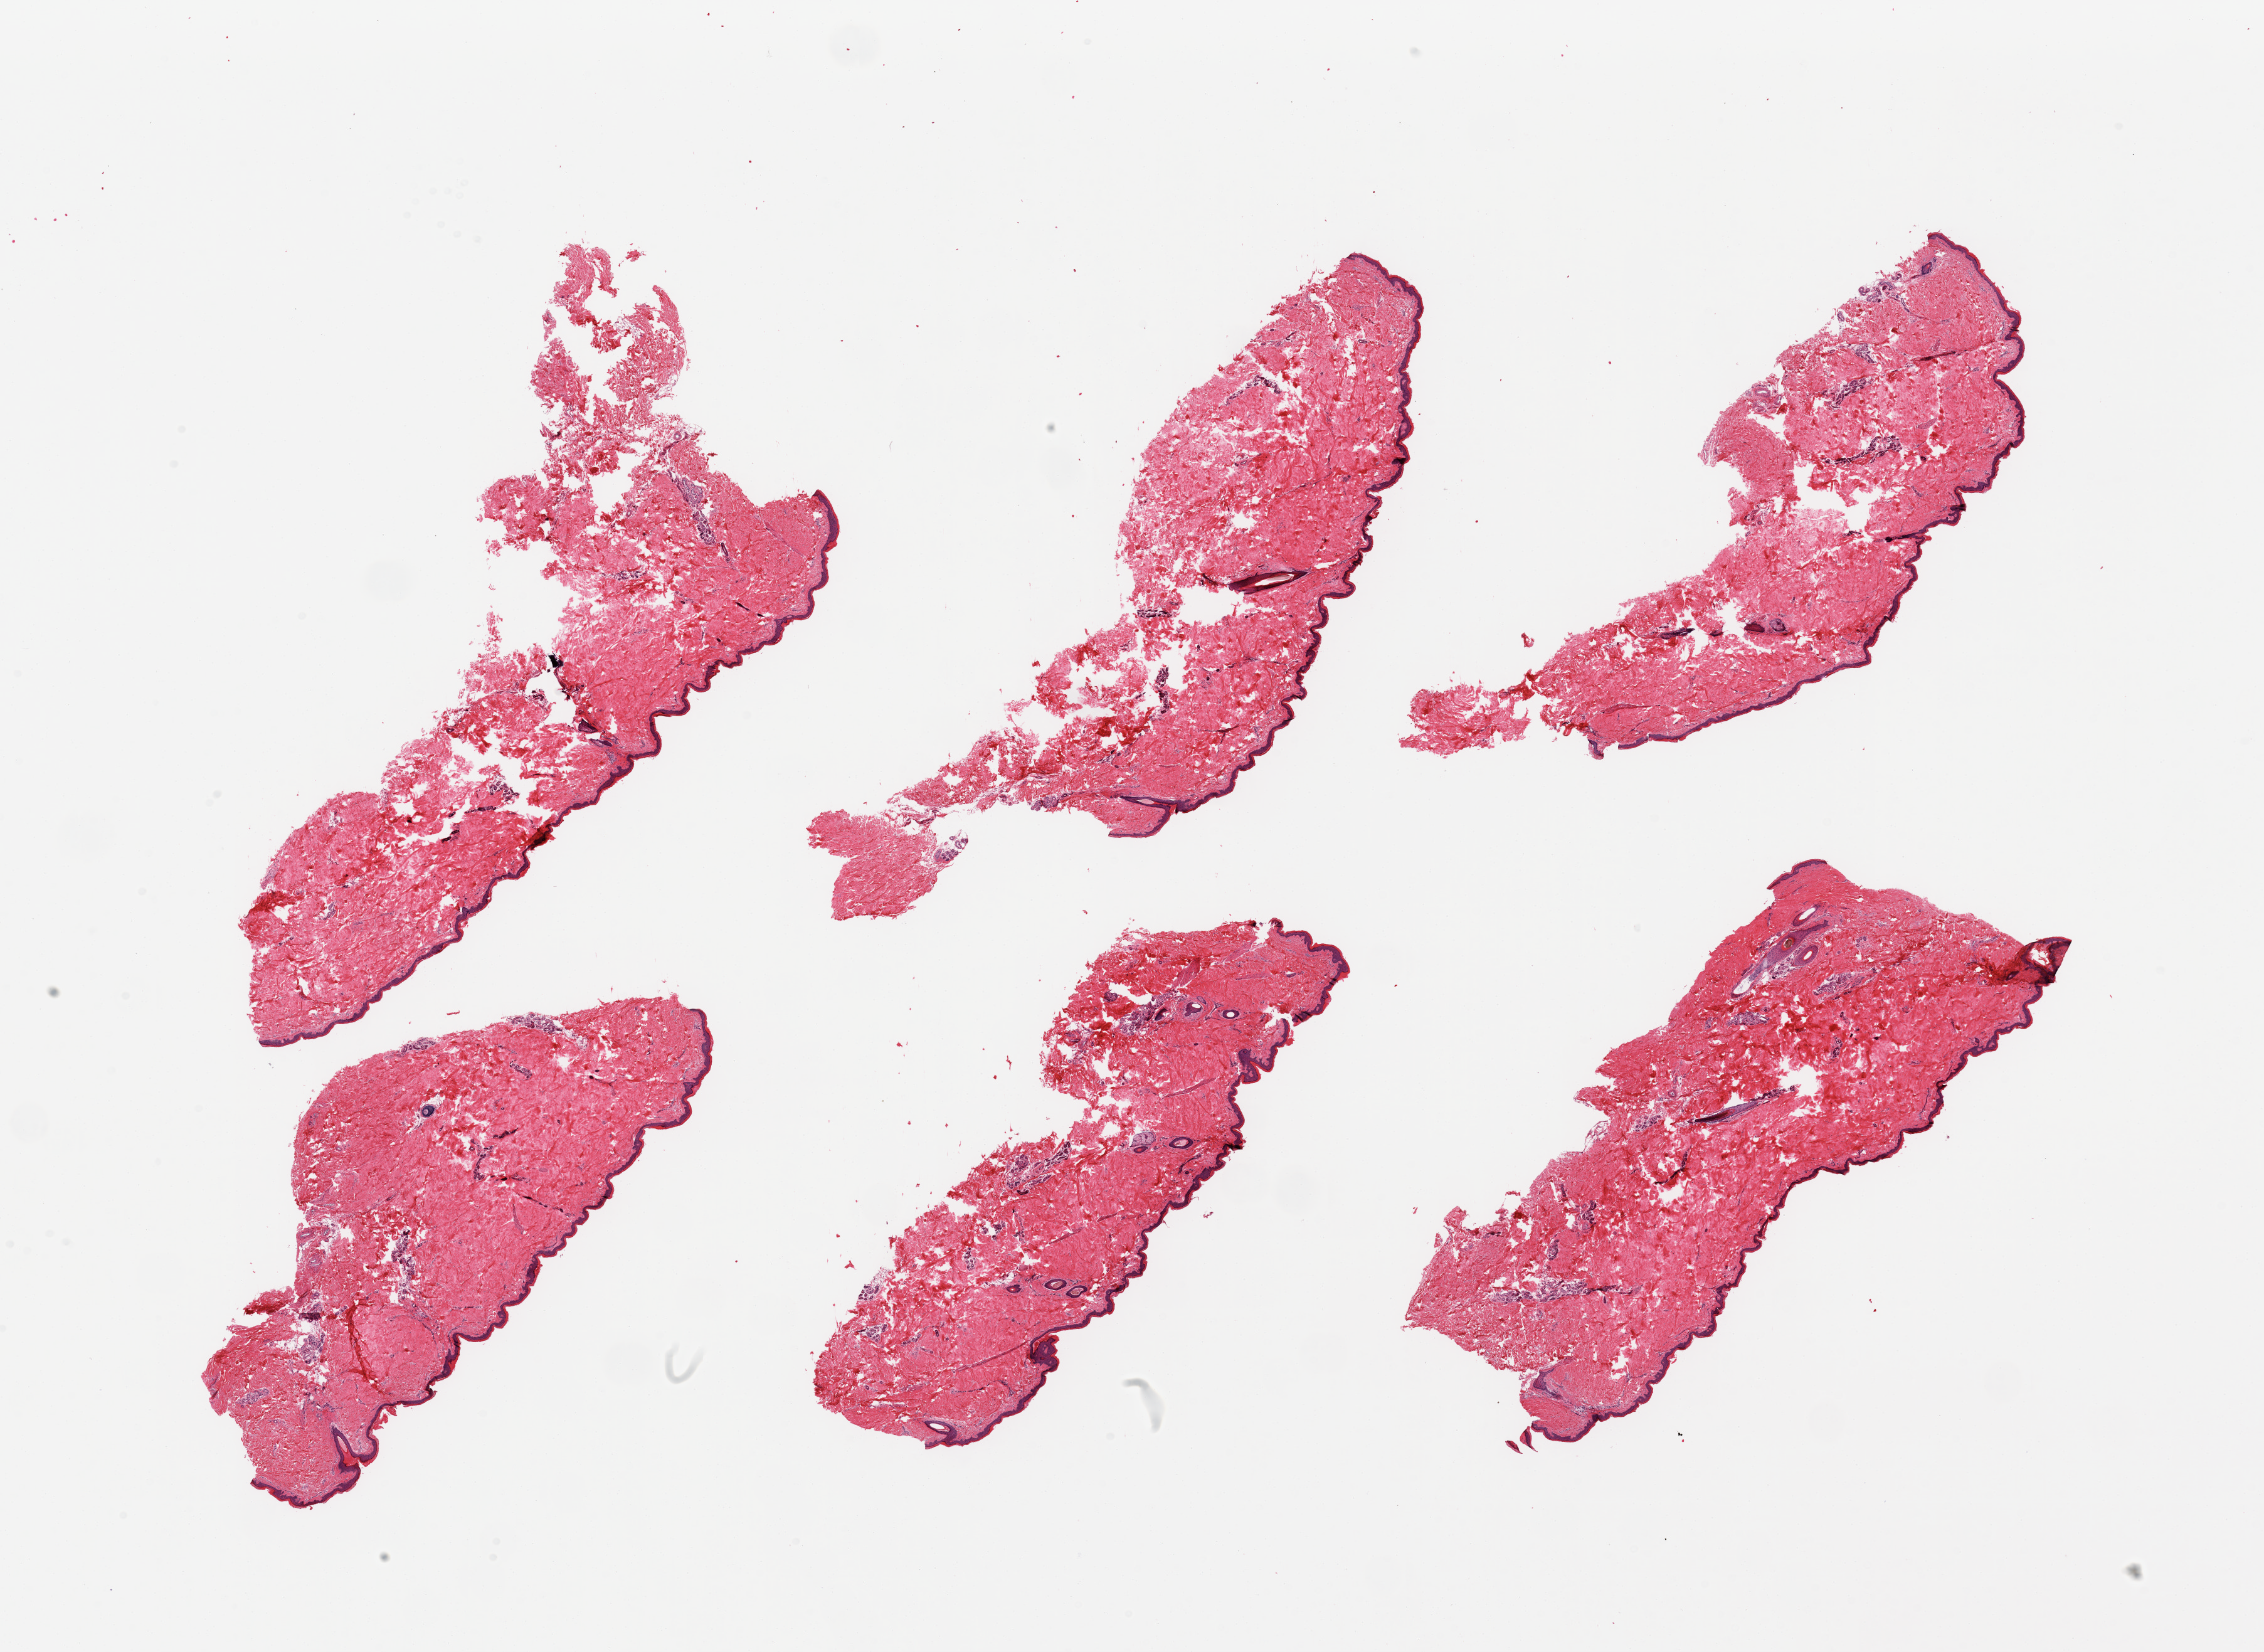
H&E whole-slide image, shown as a low-resolution overview of the whole scanned area (about 28.5 x 20.8 mm, from a 20x scan), PAXgene-fixed, paraffin-embedded tissue, section of skin of lower leg (target tissue), tissue donor sample. Male donor.
Review note (as recorded): 6 pieces, no adherent fat; squamous epithelium is ~35-45 microns.